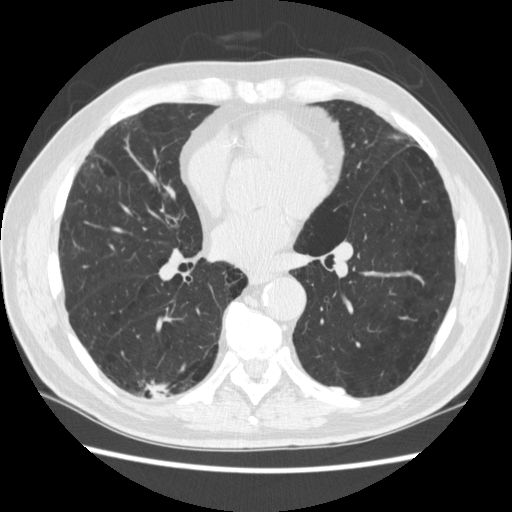
Axial slice from a low-dose chest CT screening exam, third screening round (two years after baseline), lung window (W 1500 / L -600 HU), 1.25 mm slice thickness, slice 142 of 266 in the series, 512 × 512 image matrix. Male, age 70 years at enrolment.
• Expert reader's lesion annotation, box from (x=121, y=361) to (x=185, y=421) px.
• The screening reader recorded 4 non-calcified nodules or masses ≥4 mm on this exam (right lower lobe, right lower lobe, left lower lobe, left lower lobe); which of them this box marks is not recorded.
• Participant outcome: lung cancer diagnosed 253 days after this screen — squamous cell carcinoma, NOS, right upper lobe, poorly differentiated (G3), stage IV (AJCC 6th edition).